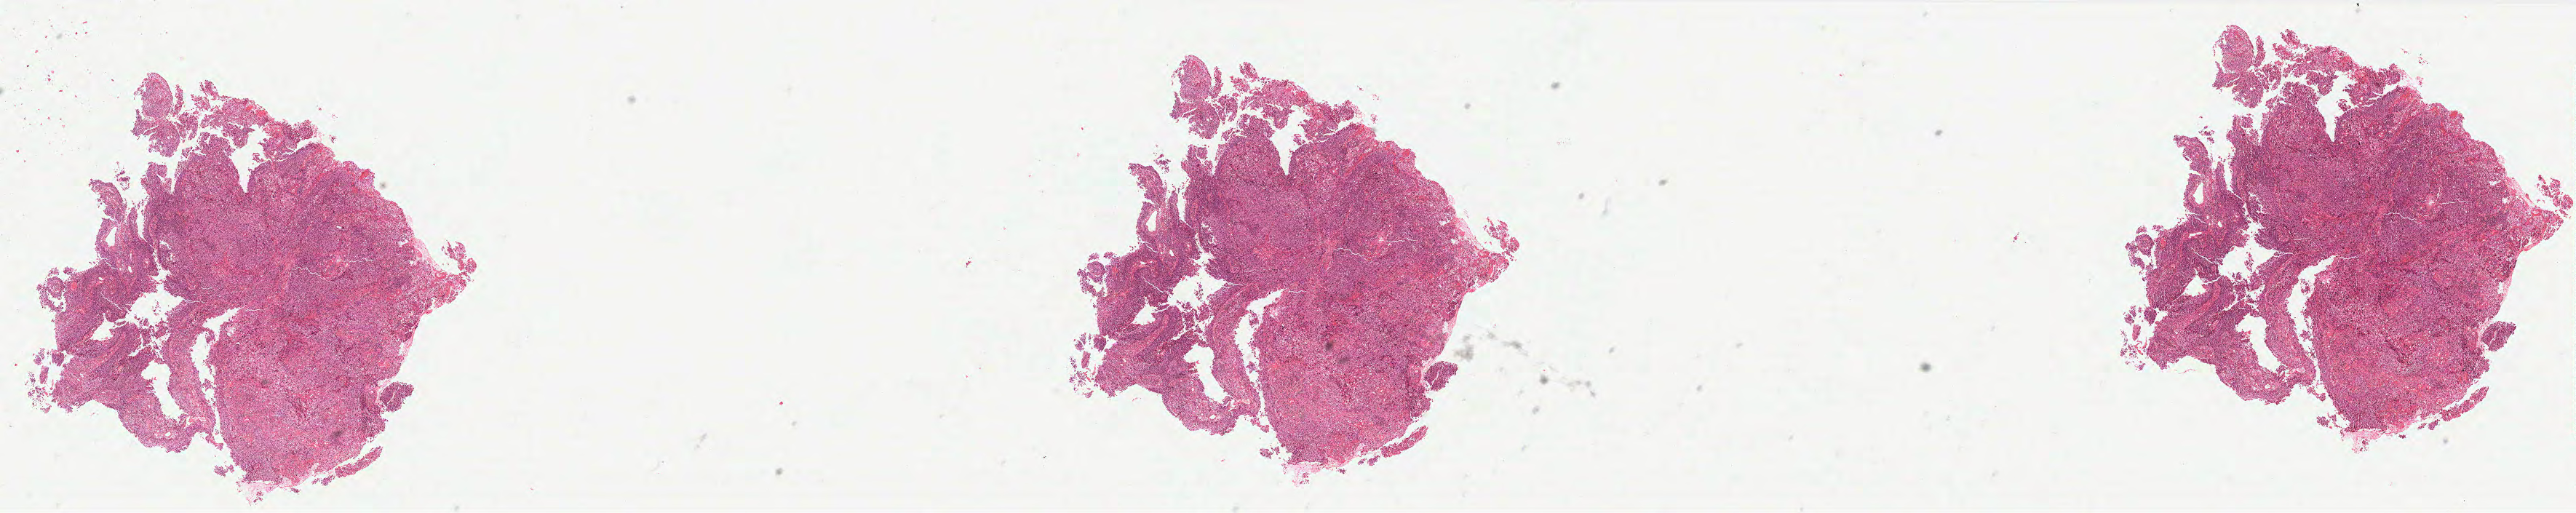
H&E-stained whole-slide image, shown as a low-resolution overview of the whole scanned area (about 28.3 x 5.6 mm), formalin-fixed paraffin-embedded (FFPE) diagnostic section, sample: primary tumour, cervix. Female patient; age at initial diagnosis 55 years. Histologic grade: G3 (poorly differentiated).
FIGO stage: IIIB. Diagnosis: Squamous cell carcinoma, NOS (cervix uteri).